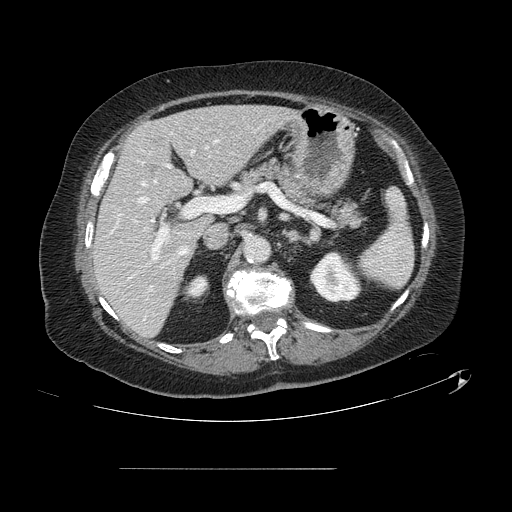
Contrast-enhanced abdominal CT, one axial slice. Slice 71 of 148 in the series (ordered by position). 120 kVp. Intravenous contrast given. Soft-tissue window (W 400 / L 40 HU). 2.5 mm slice thickness. 512 × 512 image matrix. Female patient, age 75 years. From the clinical record (not read from this slice): diagnosis: colorectal cancer liver metastases, imaged before liver resection; multiple liver metastases: no; largest metastasis: 2.4 cm; chemotherapy before resection: no.
Structures marked on this image (outlined manually by an expert reader):
- hepatic veins: box from (x=139, y=140) to (x=217, y=255) px
- liver: (x=94, y=106)–(x=293, y=336)
- planned liver remnant (the part of the liver to remain after resection): (x=94, y=106)–(x=292, y=336)
- portal vein (with intrahepatic branches): (x=133, y=151)–(x=209, y=260)